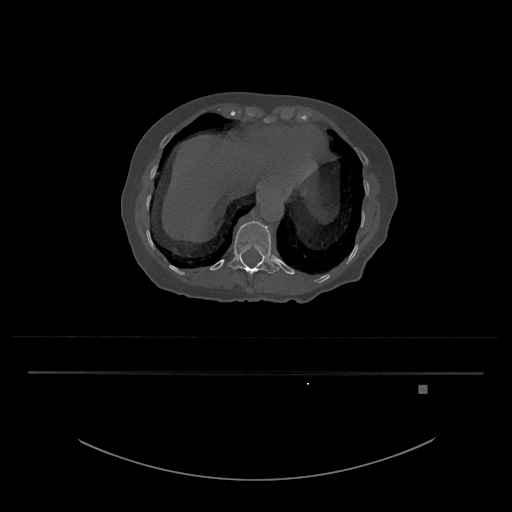
CT including the spine, one axial slice. Slice 616 of 797 in the series (ordered by position). Reconstruction kernel Br40s/3. 120 kVp. Bone window (W 1800 / L 400 HU). 0.5 mm slice thickness. 512 × 512 image matrix, field of view 500 × 500 mm. Patient: female, 57 years. Case-level facts recorded for this patient, not image findings: primary cancer: cervical.
Annotated regions visible in this slice (semi-automatic segmentation, software-assisted and operator-edited):
- T12 vertebra: bounding box (x1, y1, x2, y2) in pixels: (228, 221, 279, 276)